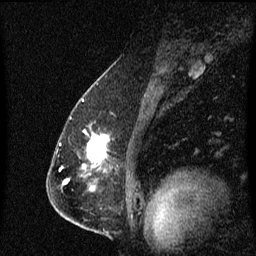
Breast MRI (dynamic contrast-enhanced), one sagittal slice; slice 41 of 60 in the series (ordered by position); dynamic contrast-enhanced series, image 2 of 3 at this slice position (ordered by acquisition); 1.5 T; TE 4.2 ms, TR 8.4 ms; 2 mm slice thickness; 256 × 256 image matrix, field of view 200 × 200 mm. Patient: female, 57 years. Case-level facts recorded for this patient, not image findings: setting: breast cancer imaged before/during neoadjuvant chemotherapy; receptor status: HR-positive, HER2-negative.
Annotated regions visible in this slice (semi-automatic segmentation, software-assisted and operator-edited):
- analysis volume of interest (the breast-tissue region the enhancement analysis was run in; not a lesion): bounding box <70,118,111,175> (left, top, right, bottom; pixels)
- tumour enhancement mask (voxels above the 70 % enhancement threshold inside the analysis volume of interest): <88,134,108,167>